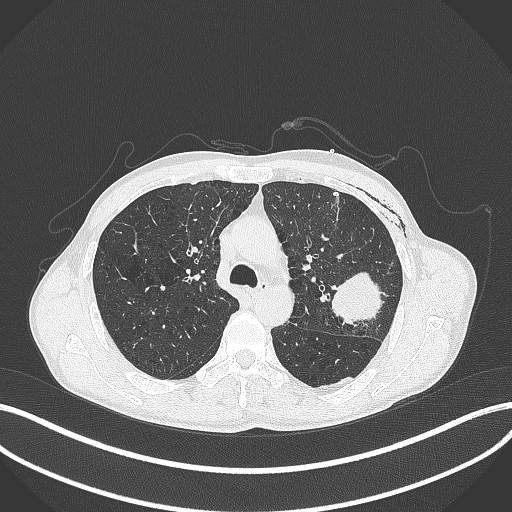
Chest CT, one axial slice; position 276 of 457 along the scan axis; 120 kVp; lung window (W 1500 / L -600 HU); 1 mm slice thickness; 512 × 512 image matrix. Patient: male, 58 years. Case-level facts recorded for this patient, not image findings: clinical TNM (as recorded): T3 N0 M0.
Annotated regions visible in this slice (bounding box drawn by a radiologist):
- lung tumour (recorded histology: adenocarcinoma): box from (x=327, y=265) to (x=387, y=328) px